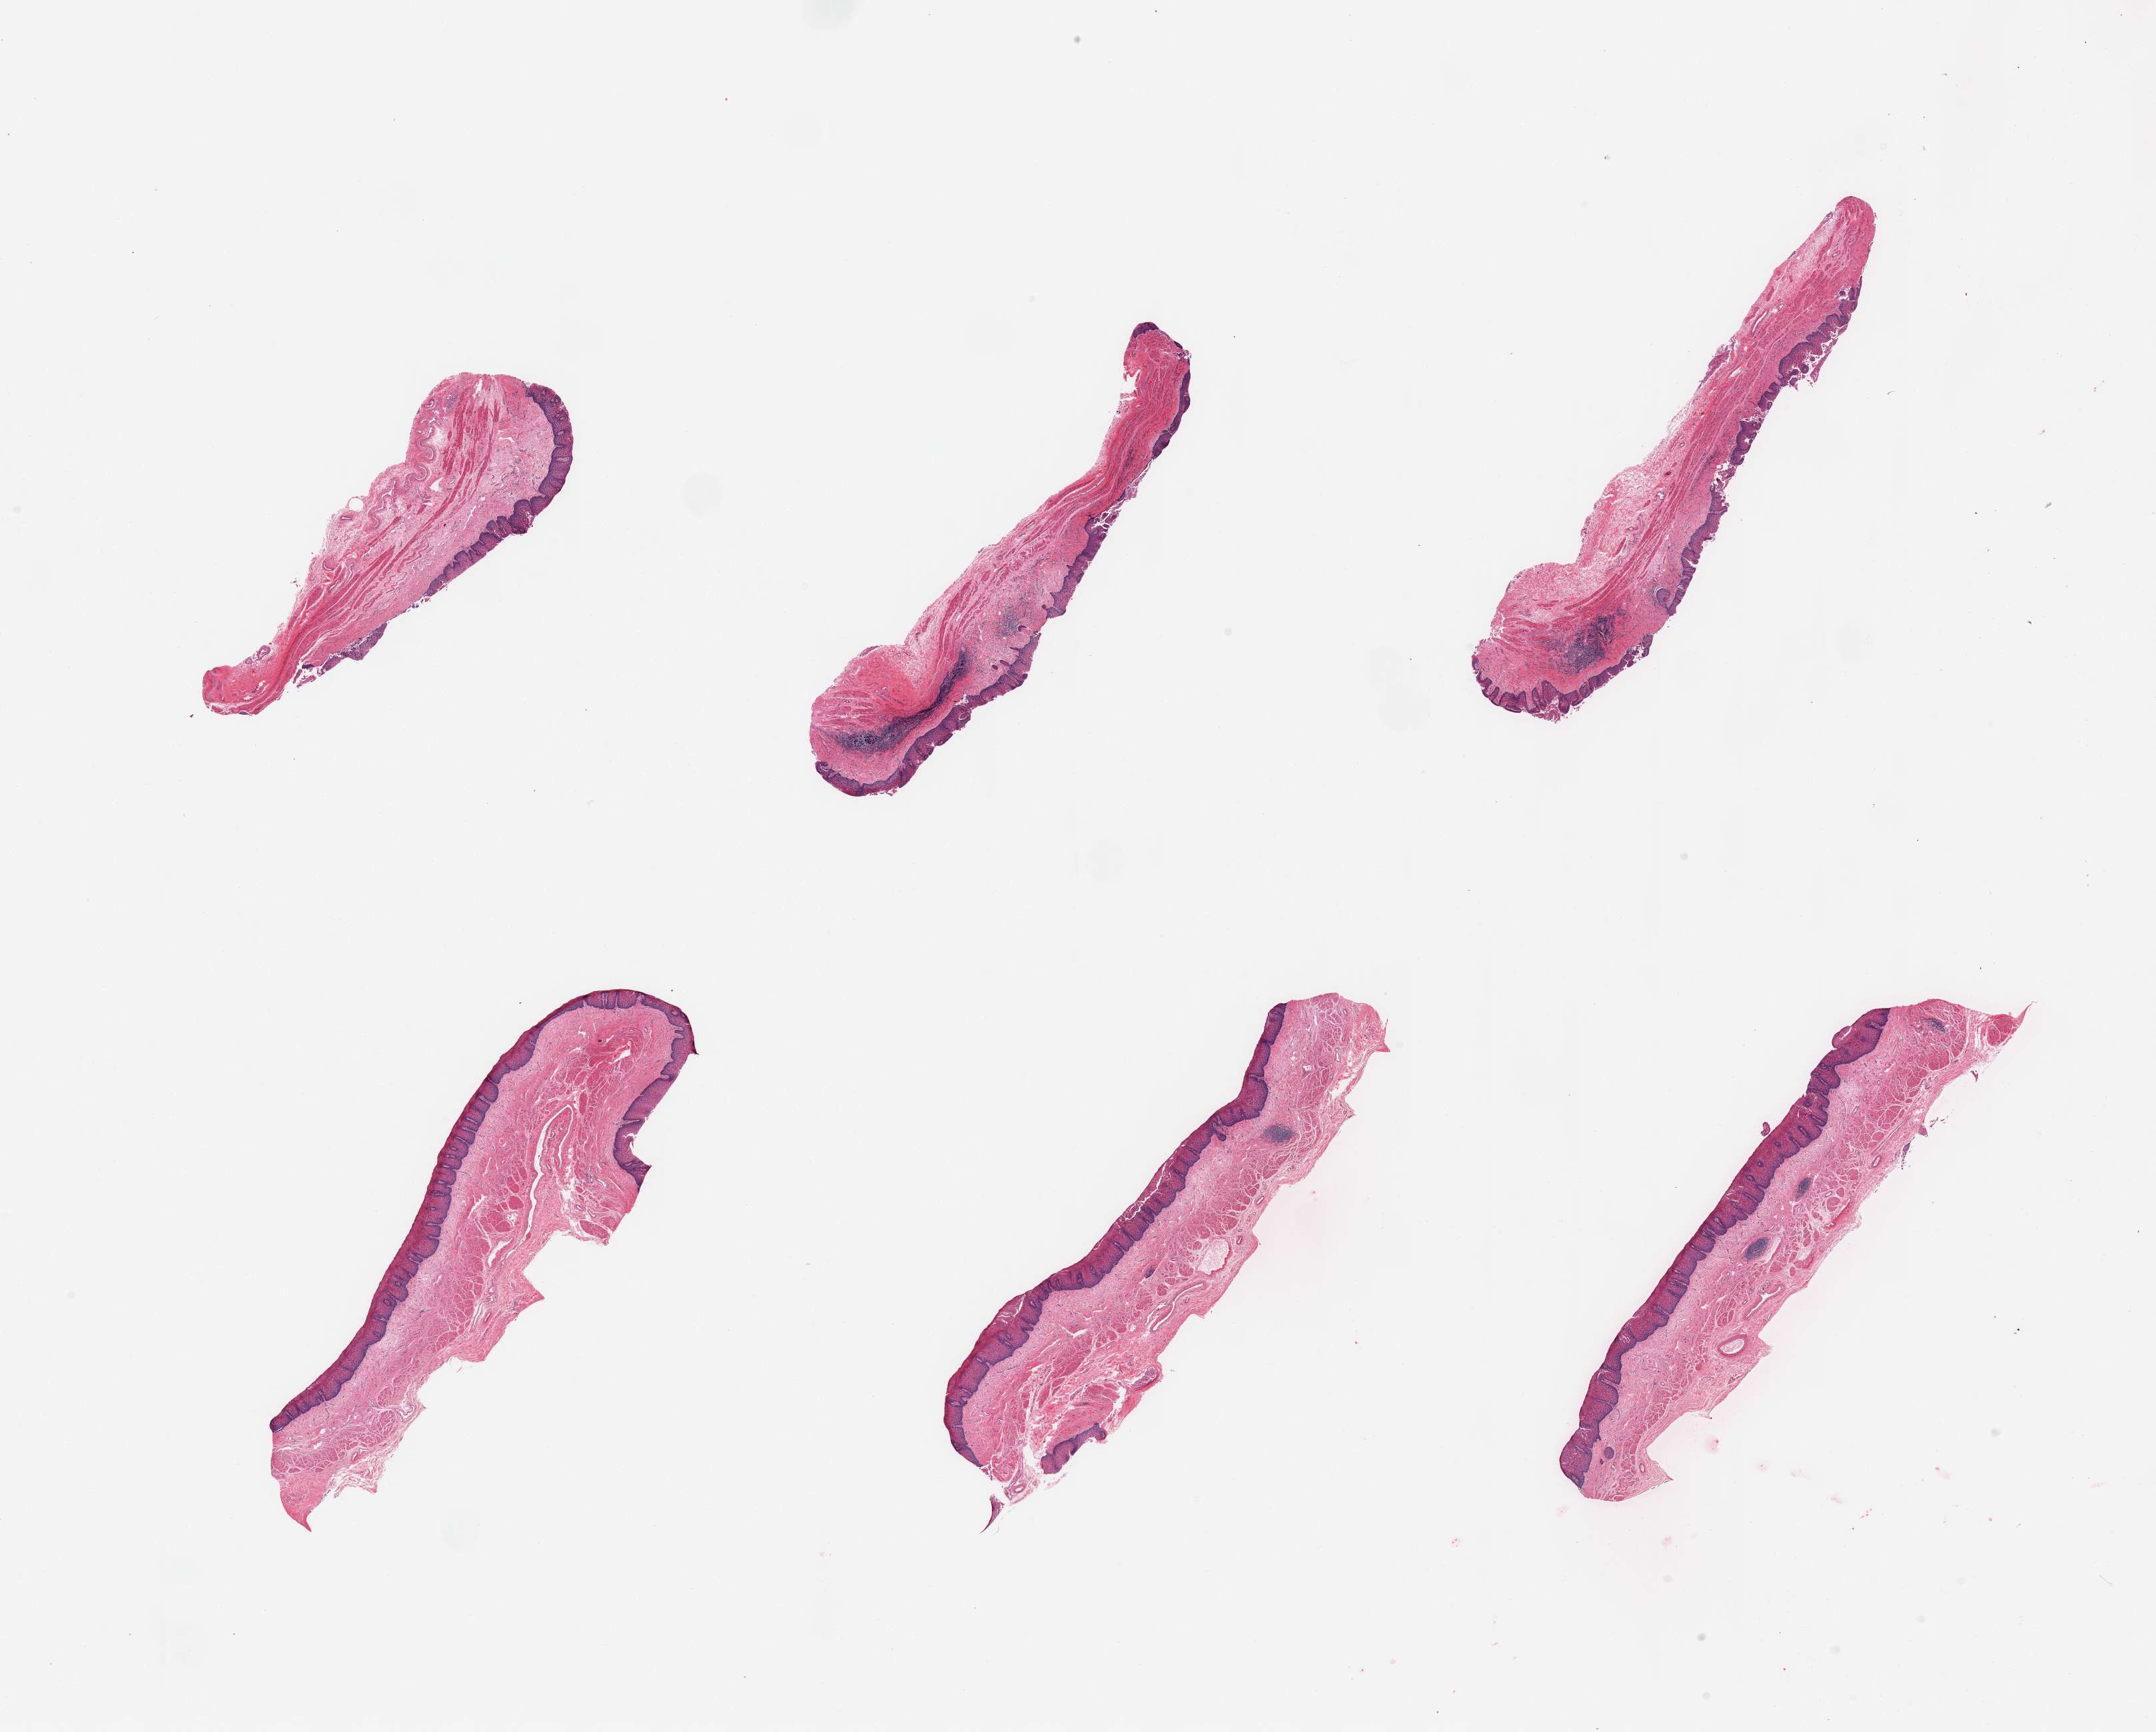
Hematoxylin and eosin (H&E) whole-slide image, brightfield, whole scanned area (about 25.6 x 20.6 mm, slide scanned at 20x) shown as a low-resolution overview. PAXgene-fixed paraffin-embedded (PFPE) section. Target tissue: esophageal mucous membrane. Tissue donor sample. Donor: male.
Review note (as recorded): 6 pieces, squamous mucosa is ~0.3mm, ~20% thickness.